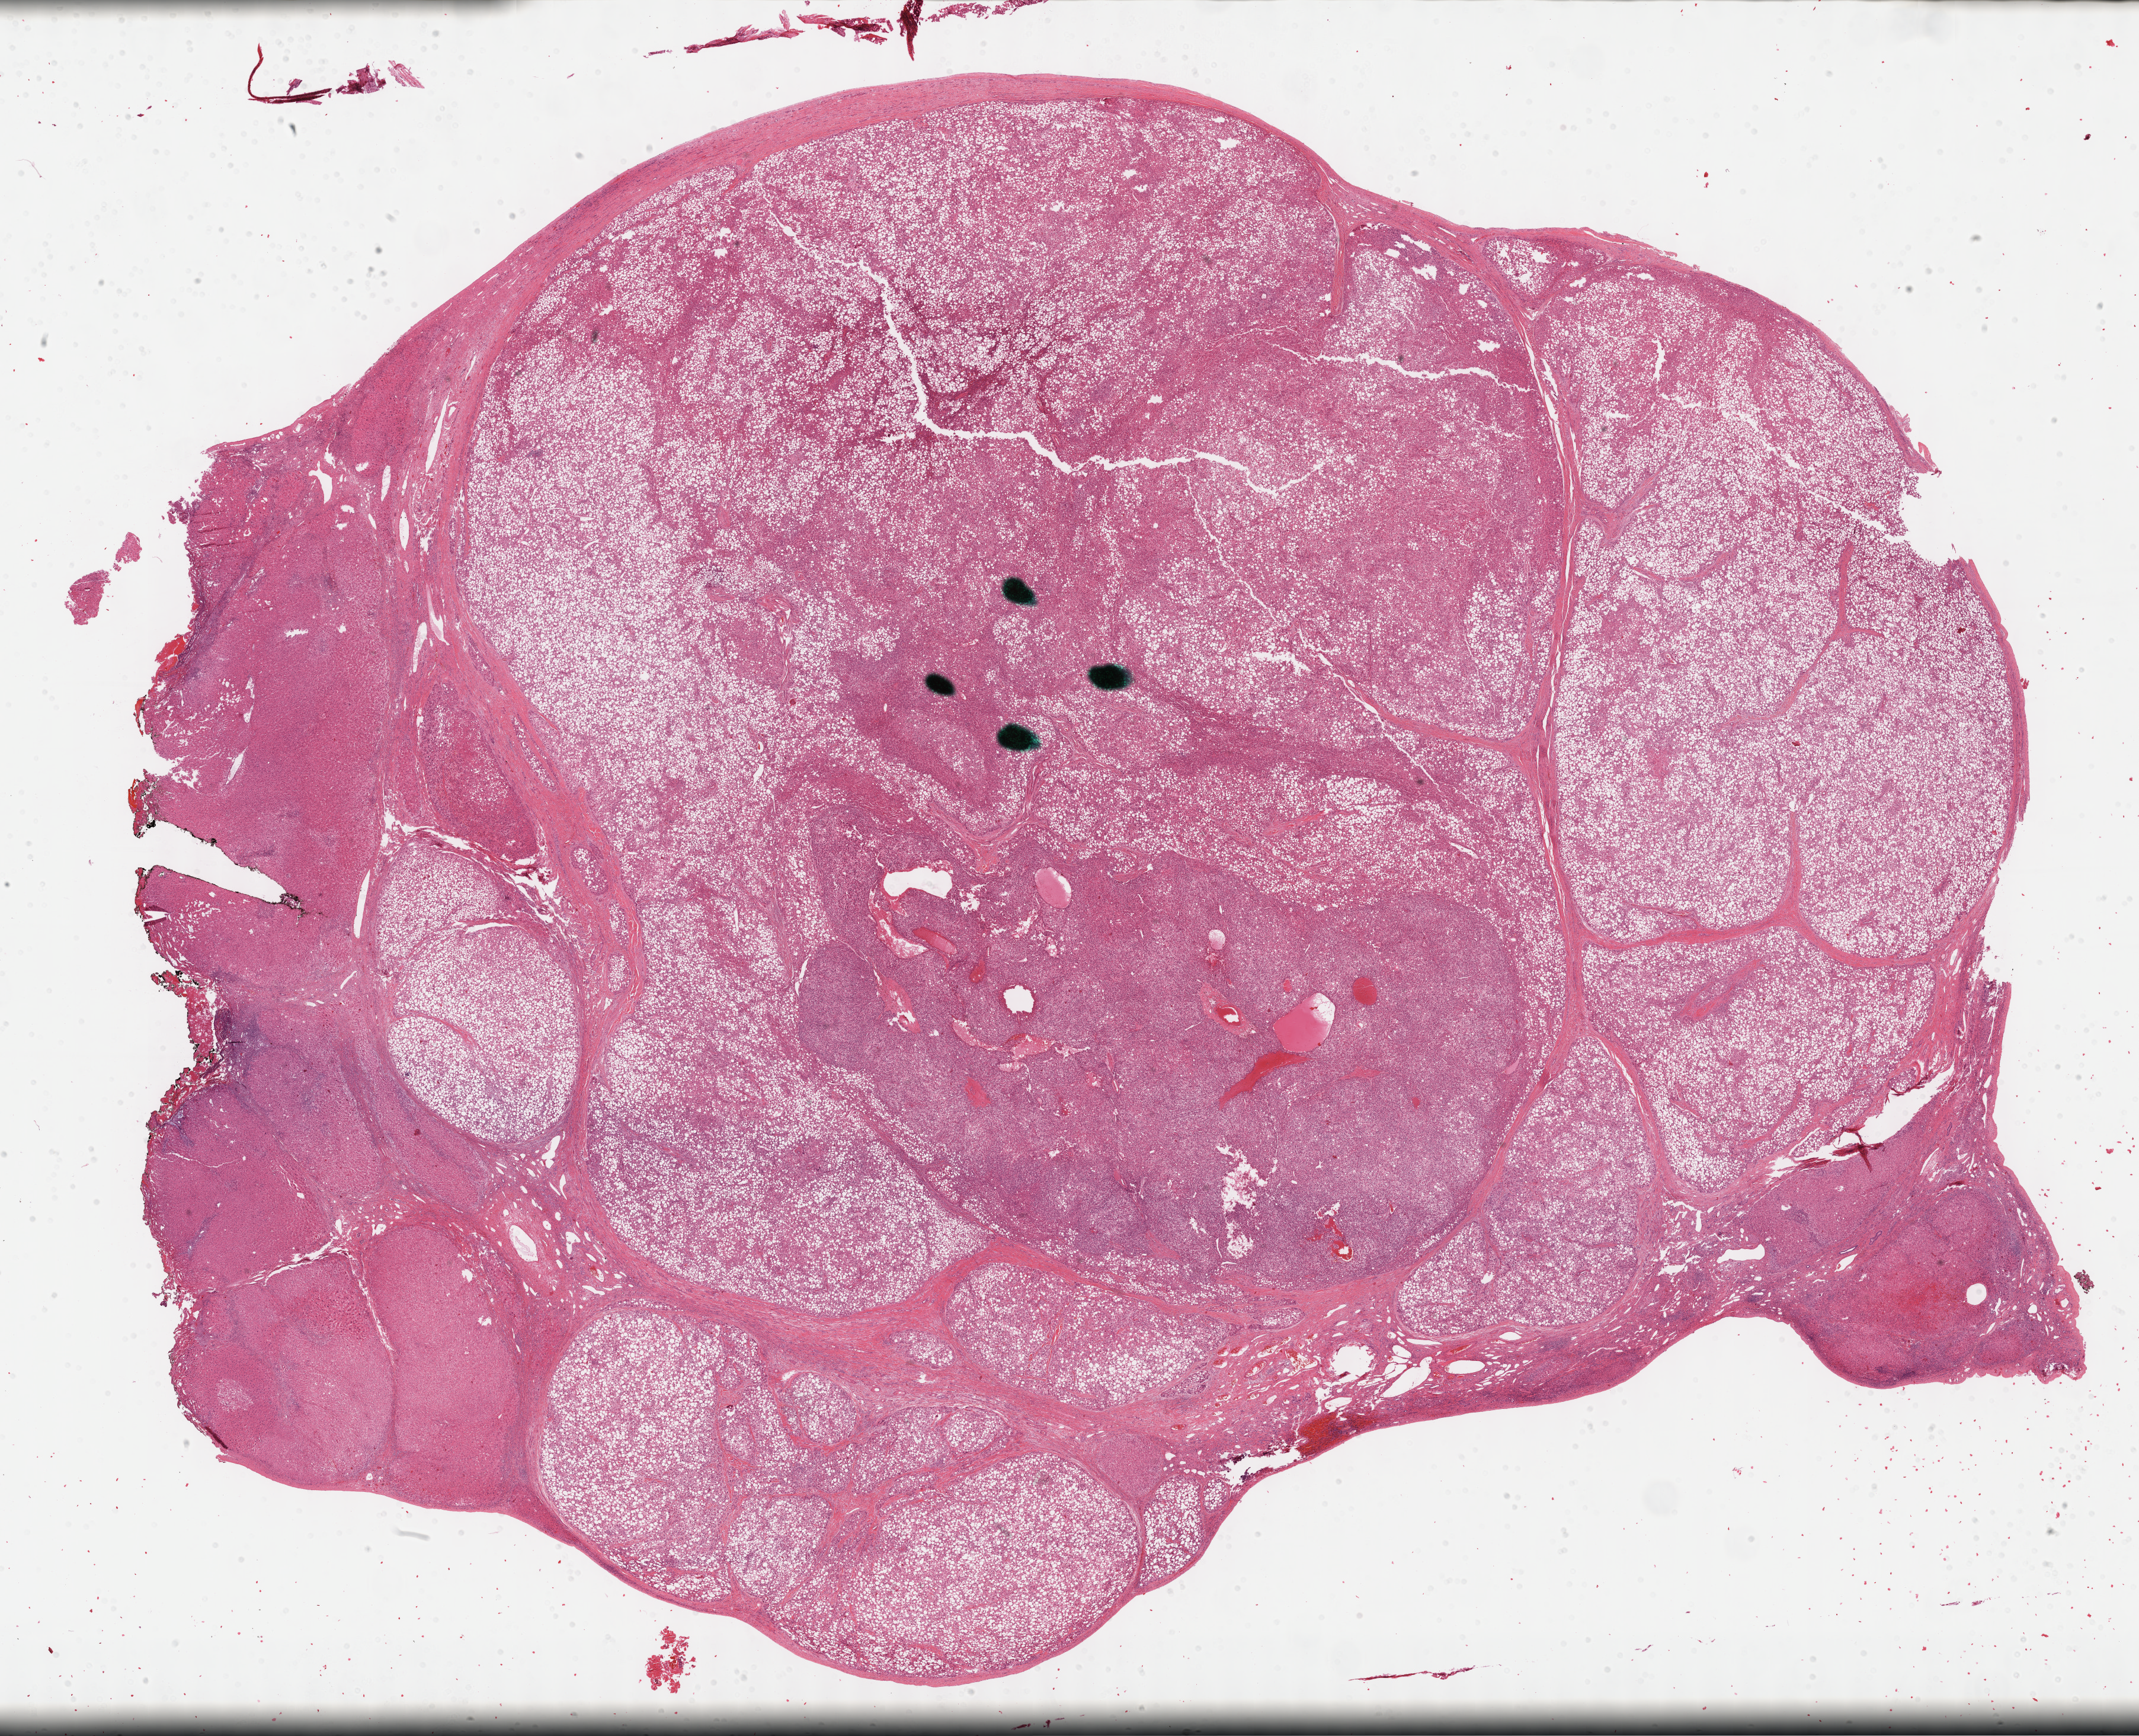
Digitized H&E tissue section (whole slide) — low-resolution overview of the scanned area, about 29.2 x 23.7 mm (from a 40x scan); formalin-fixed paraffin-embedded (FFPE) diagnostic section; liver, primary tumour sample. Patient: female, age at initial diagnosis 66 years. Histologic grade: G1 (well differentiated).
Histologic diagnosis: Hepatocellular carcinoma, NOS.